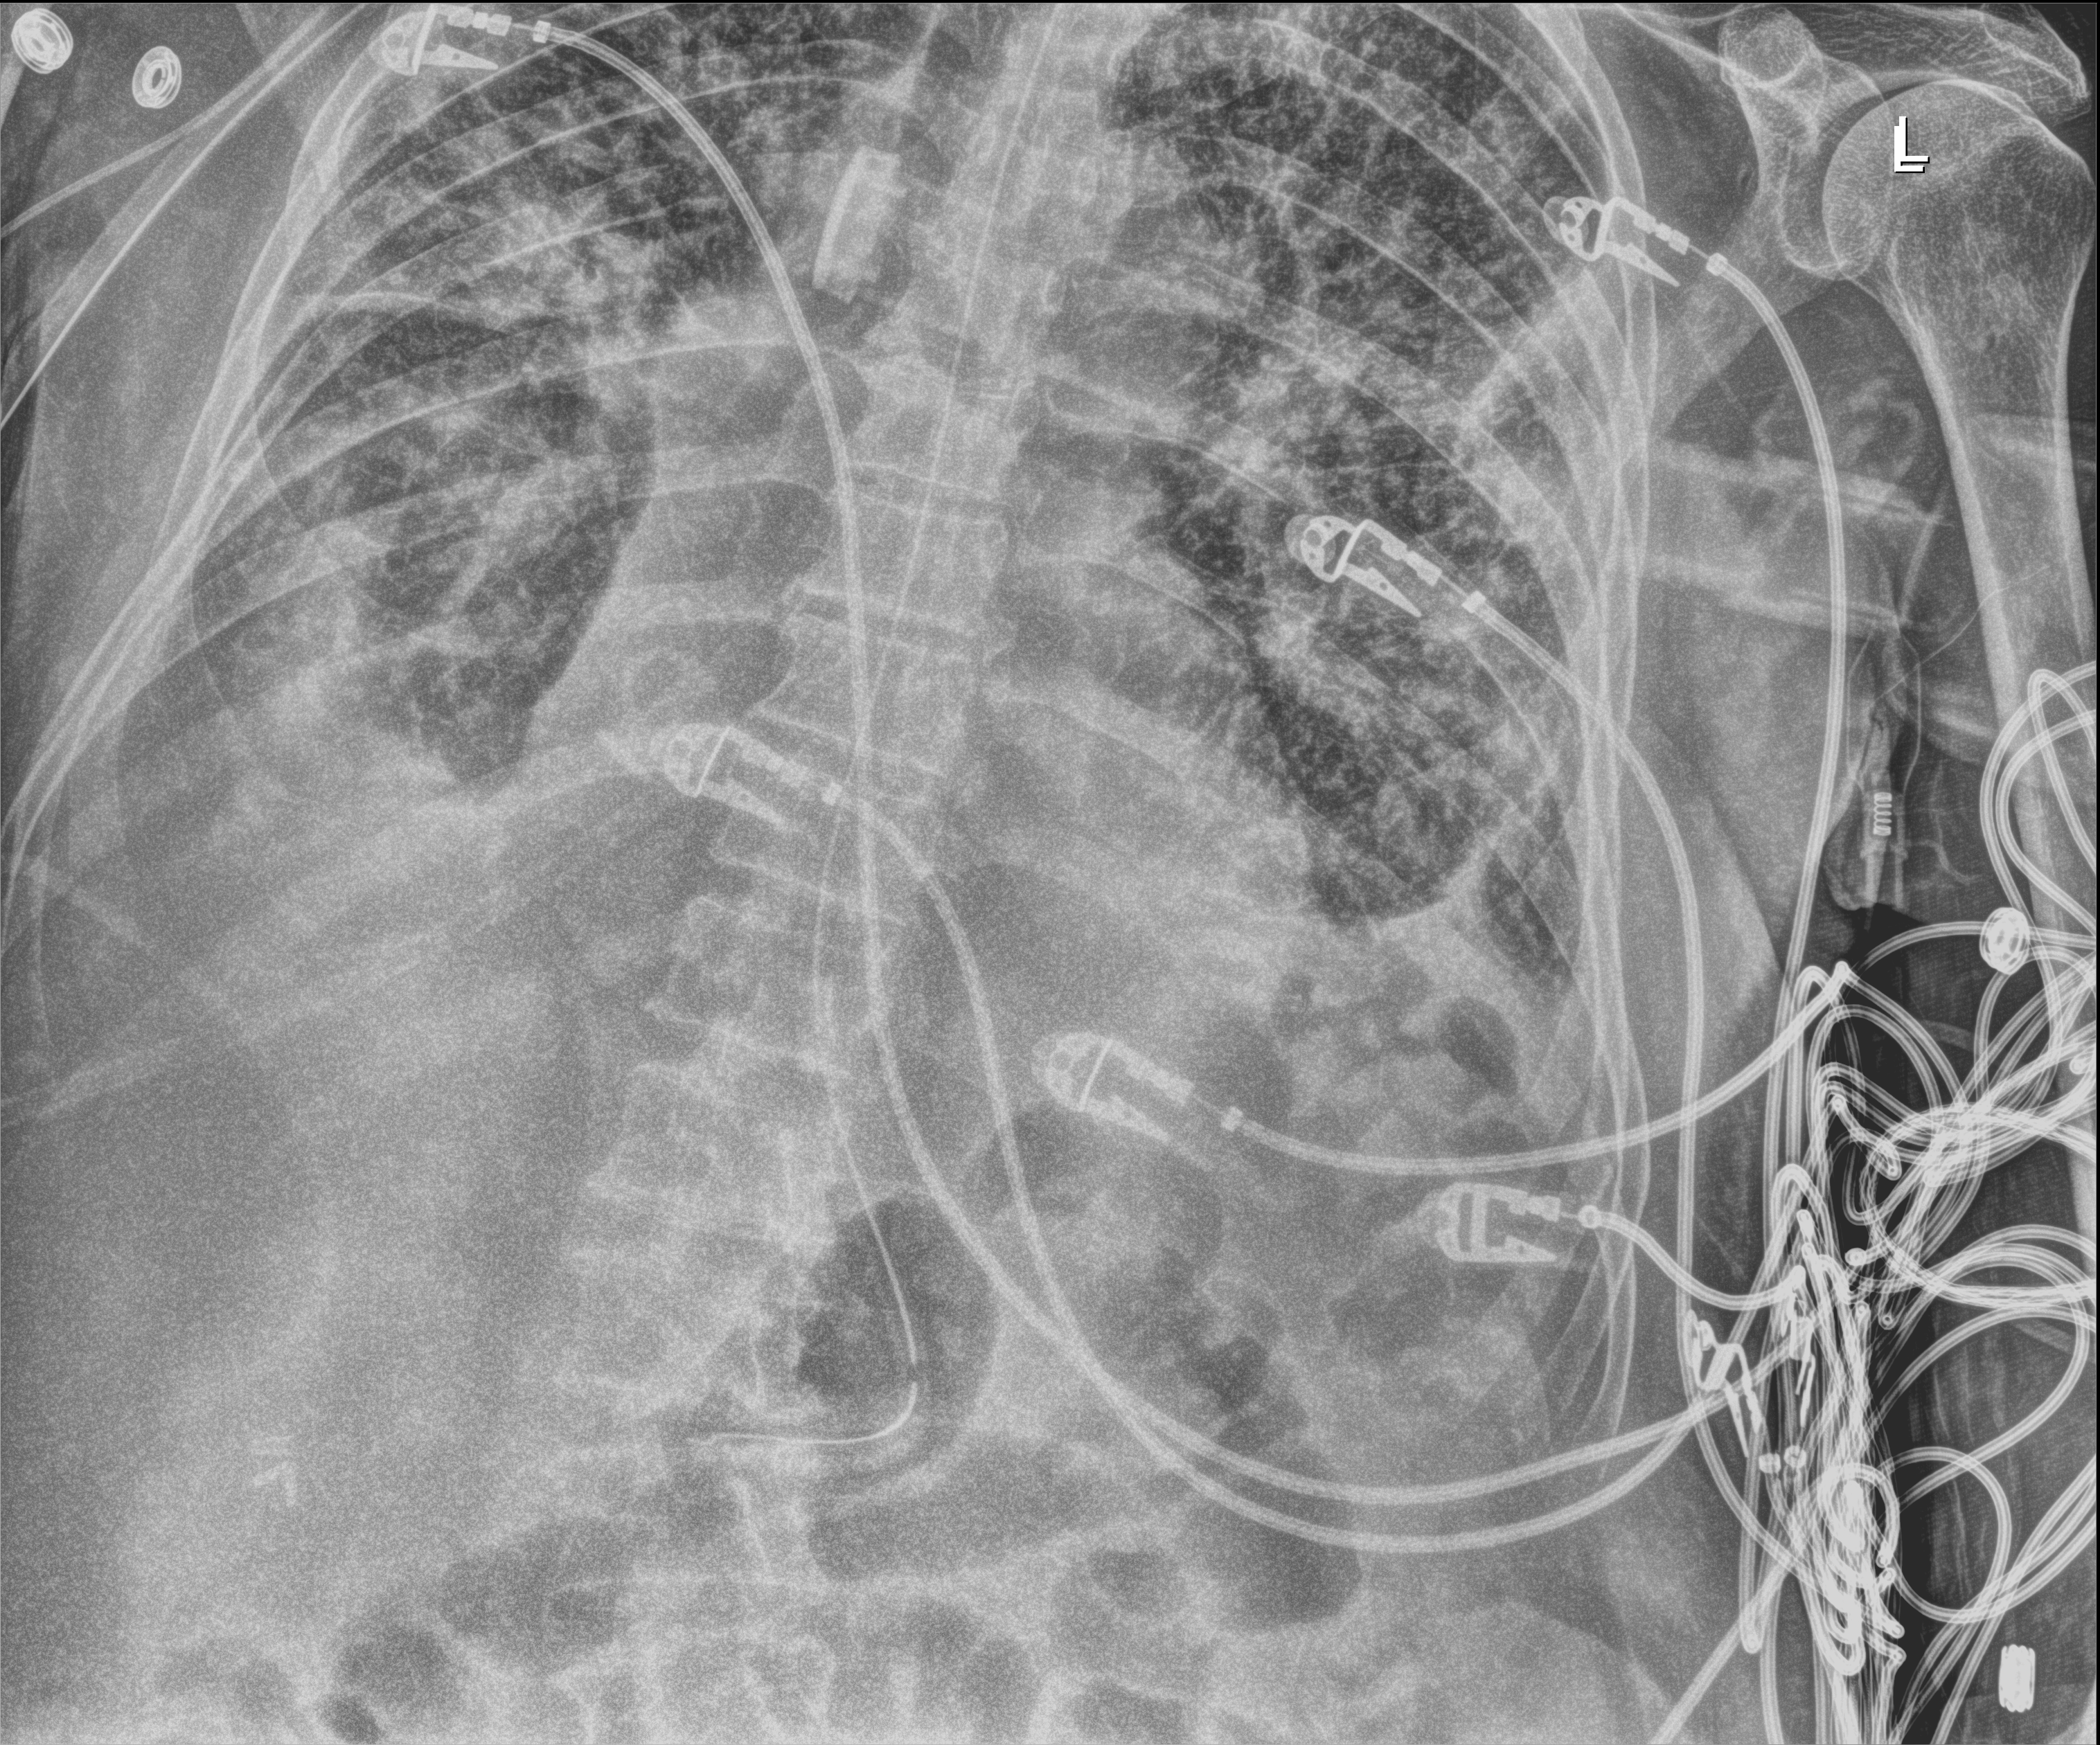
Portable chest radiograph, anteroposterior (AP) projection. Male patient hospitalised with COVID-19, age 75–90 years.
Hospital-stay facts (about this admission, not read from this image; timing relative to this image not recorded): admitted to intensive care during this hospital stay: yes.